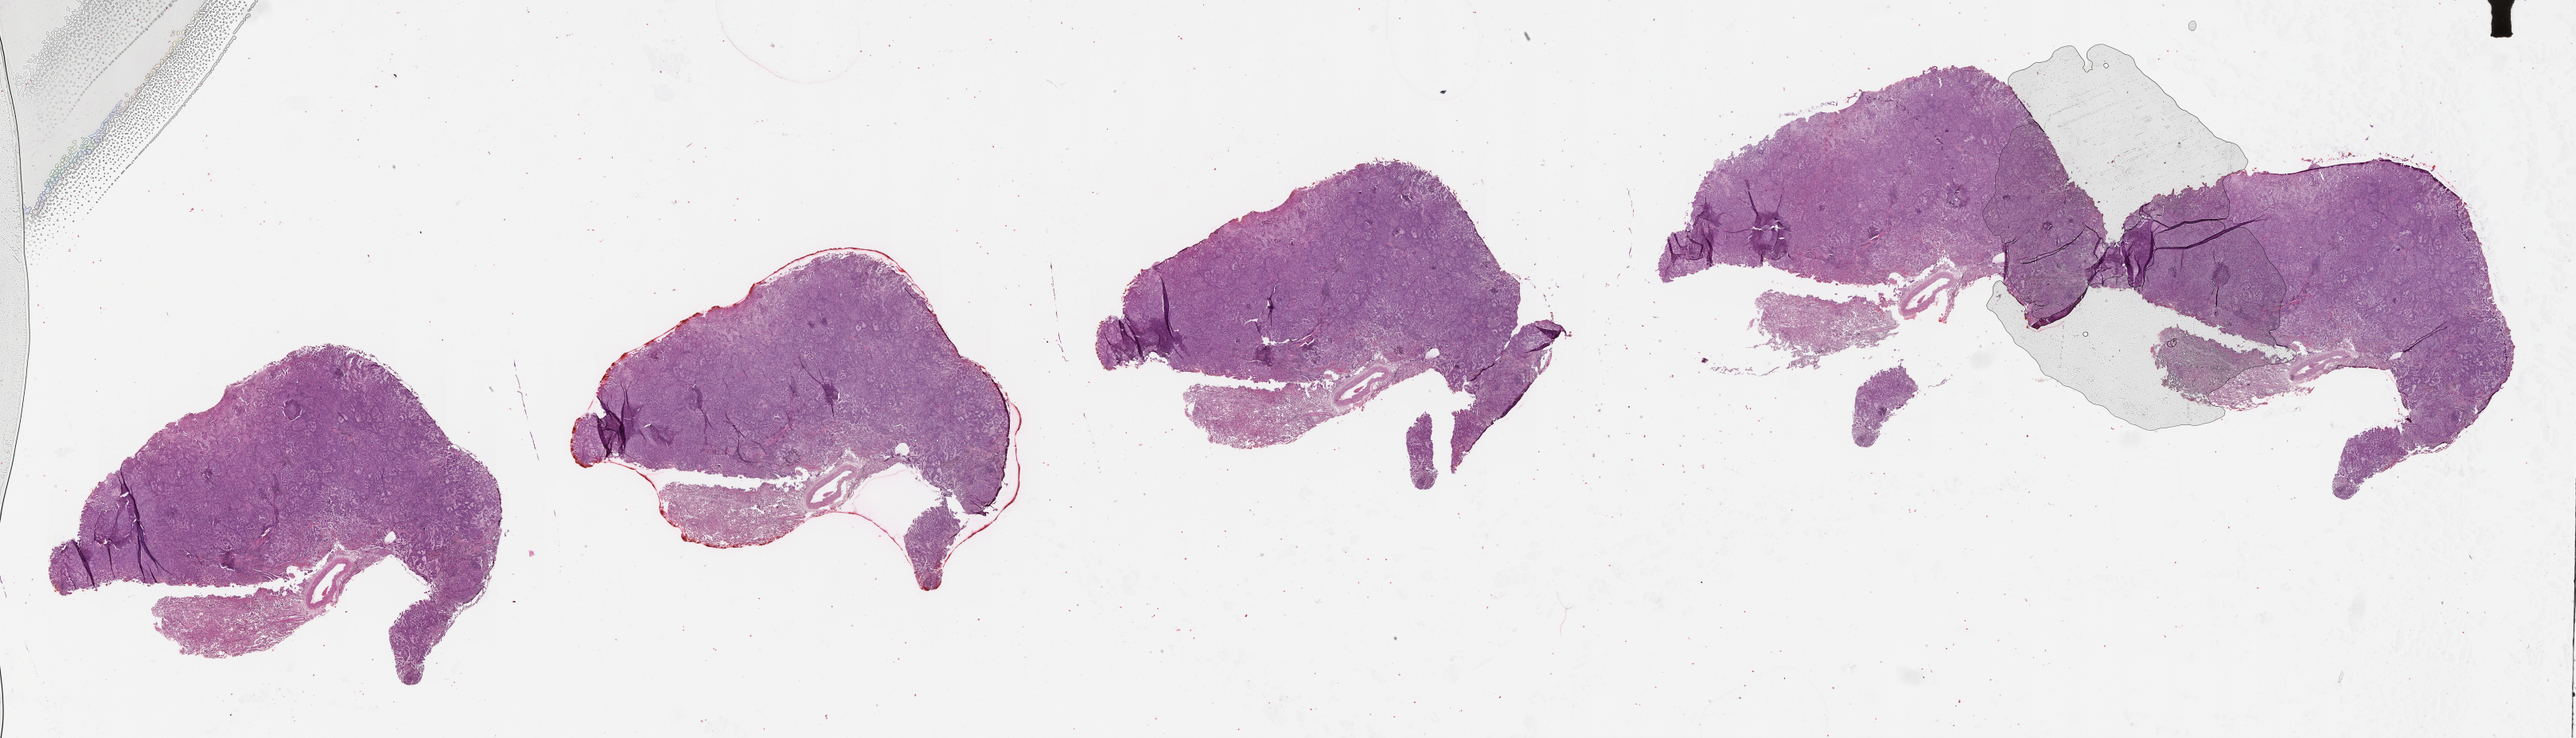
Hematoxylin and eosin (H&E) stained whole-slide image, a low-resolution overview of the entire scanned area, about 52.1 x 14.9 mm (from a 20x scan), lung, tissue type not recorded.
* patient diagnosis (cohort enrolment): lung adenocarcinoma (lung)